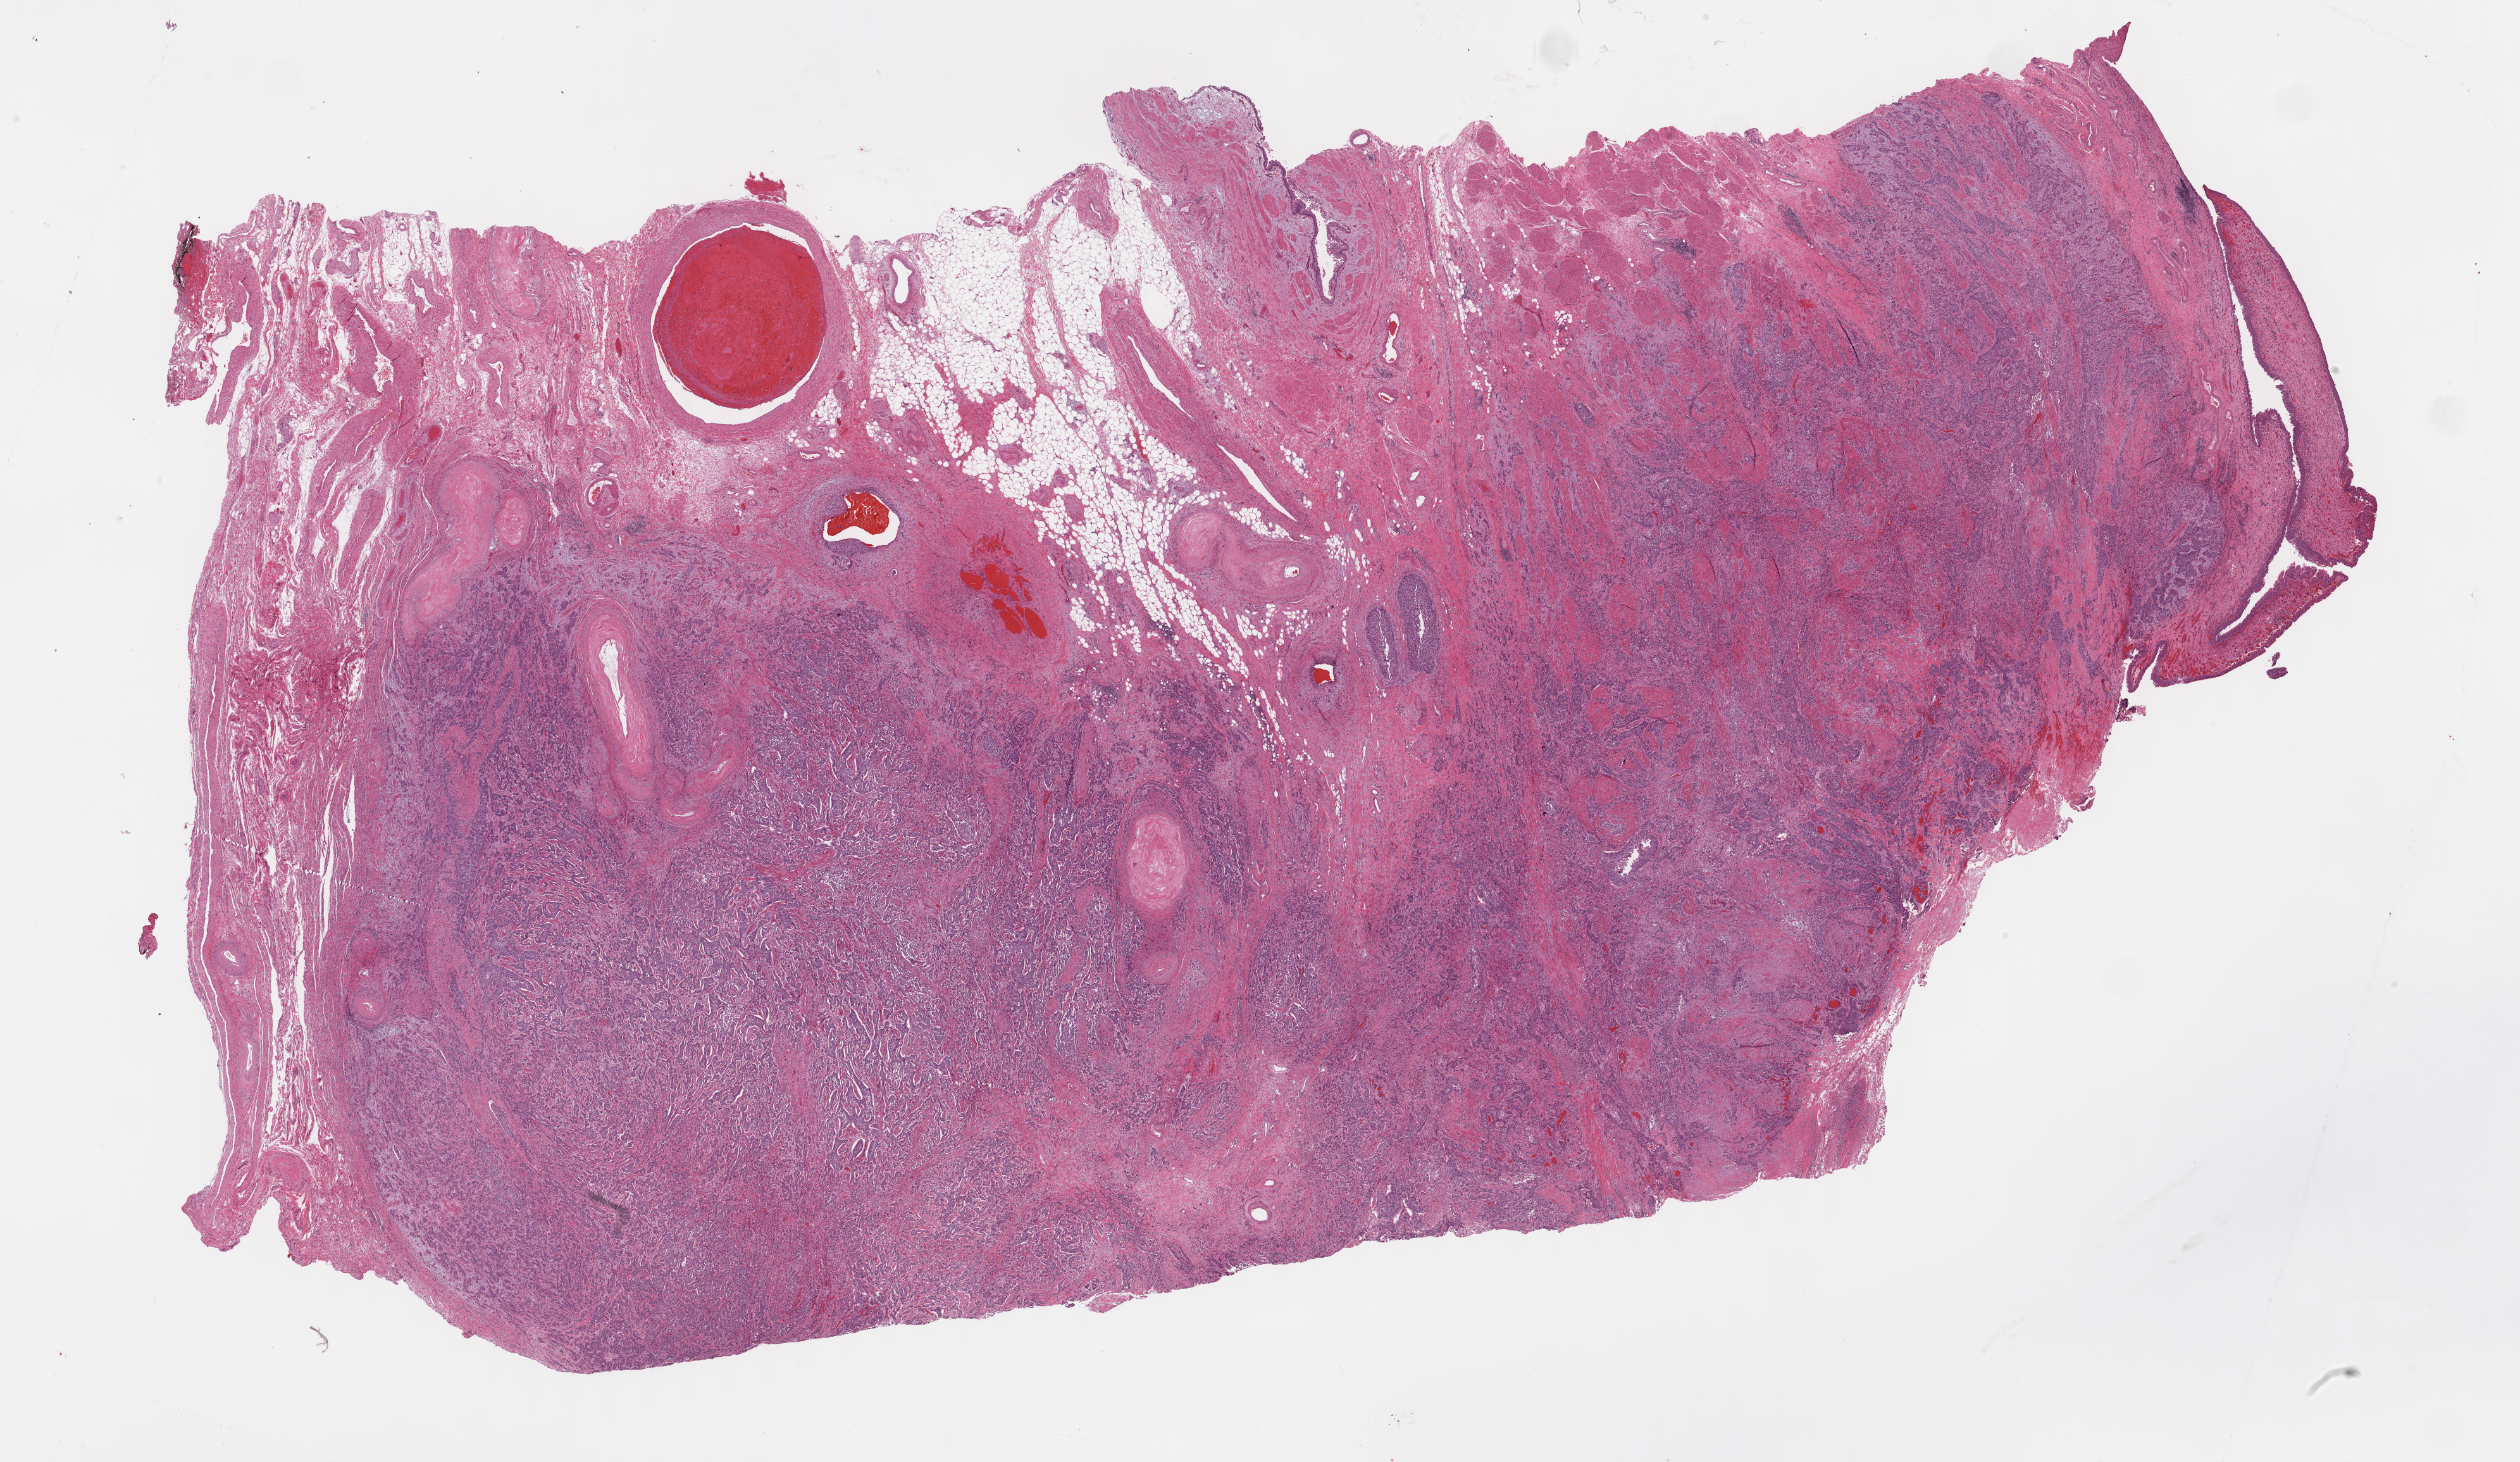
Digitized H&E-stained tissue section (whole slide), low-resolution overview of the scanned area, about 32.2 x 18.7 mm. FFPE section. Sample: primary tumour, bladder. Patient: female, age at initial diagnosis 79 years. Histologic grade: high grade.
• lymph nodes positive (case pathology): 0 of 16 examined
• AJCC pathologic stage: III
• diagnosis: Transitional cell carcinoma (posterior wall of bladder)